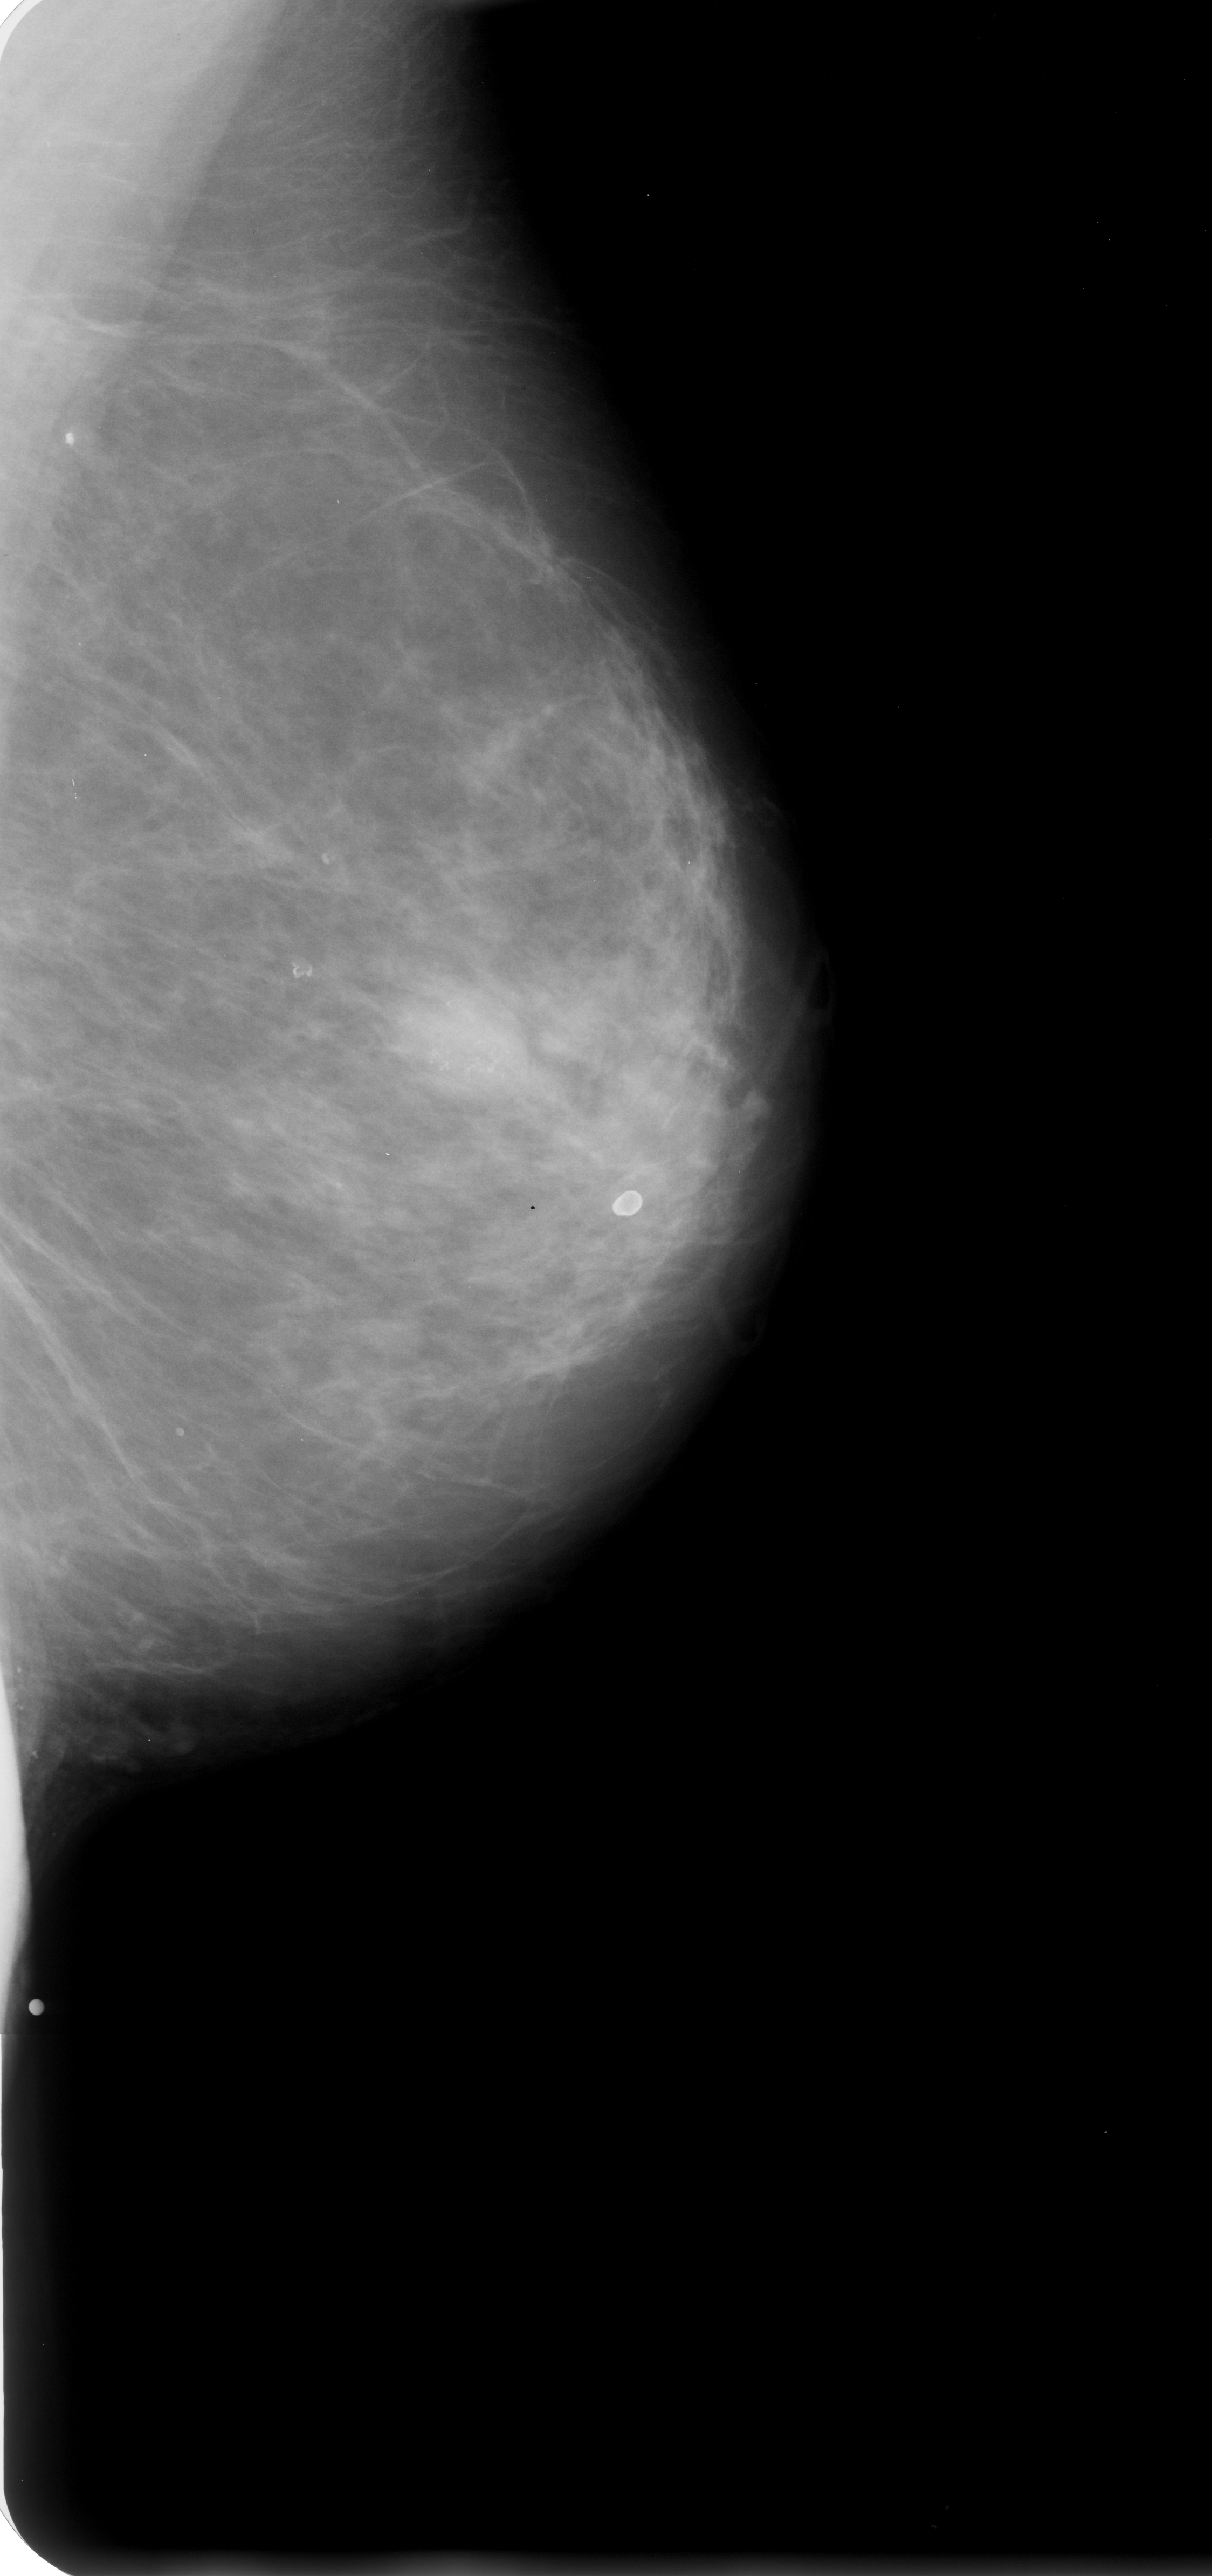
Digitized screen-film mammogram, left breast, mediolateral oblique (MLO) view, BI-RADS breast density category 2 (scale 1–4).
Marked abnormality: calcifications, morphology pleomorphic, distribution clustered; BI-RADS assessment category 4; subtlety rating 4 on a 1 (subtle) to 5 (obvious) scale; pathology result (as recorded, not read from the image): benign.